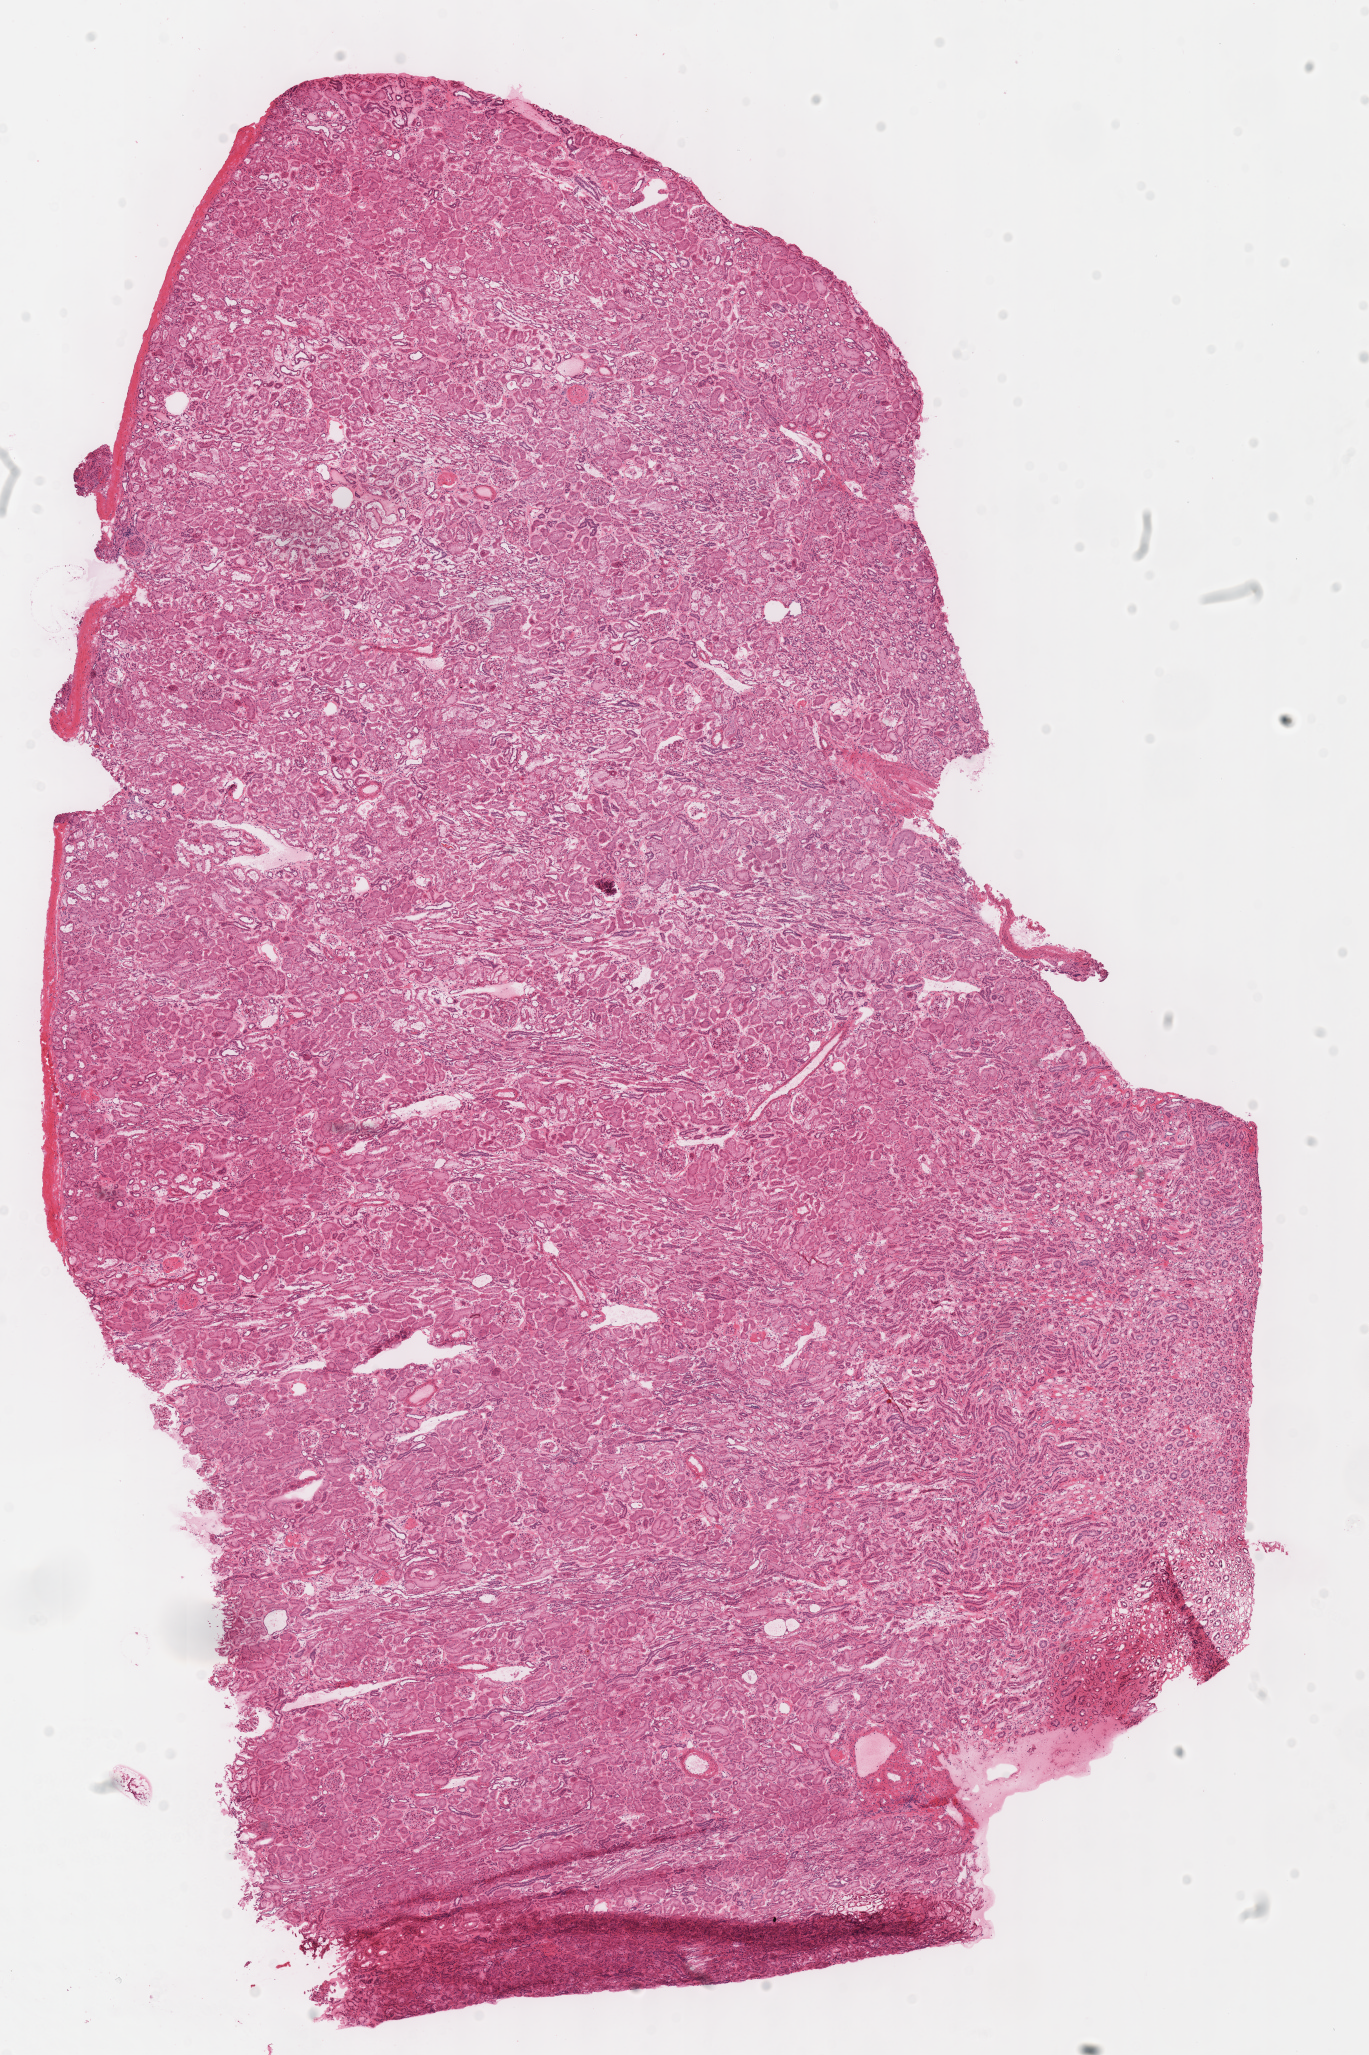
Digitized H&E tissue section (whole slide) — whole scanned area (about 10.8 x 16.2 mm, acquisition: 40x scan) shown as a low-resolution overview; frozen section from the top of the tissue portion; kidney, solid tissue normal (non-tumour tissue) sample. Female, age 44 years at initial diagnosis. Inflammatory infiltration, as recorded: lymphocyte infiltration 0%, monocyte infiltration 0%, neutrophil infiltration 0%.
- this section: solid tissue normal (non-tumour) sample from the same patient
- patient diagnosis: Renal cell carcinoma, chromophobe type